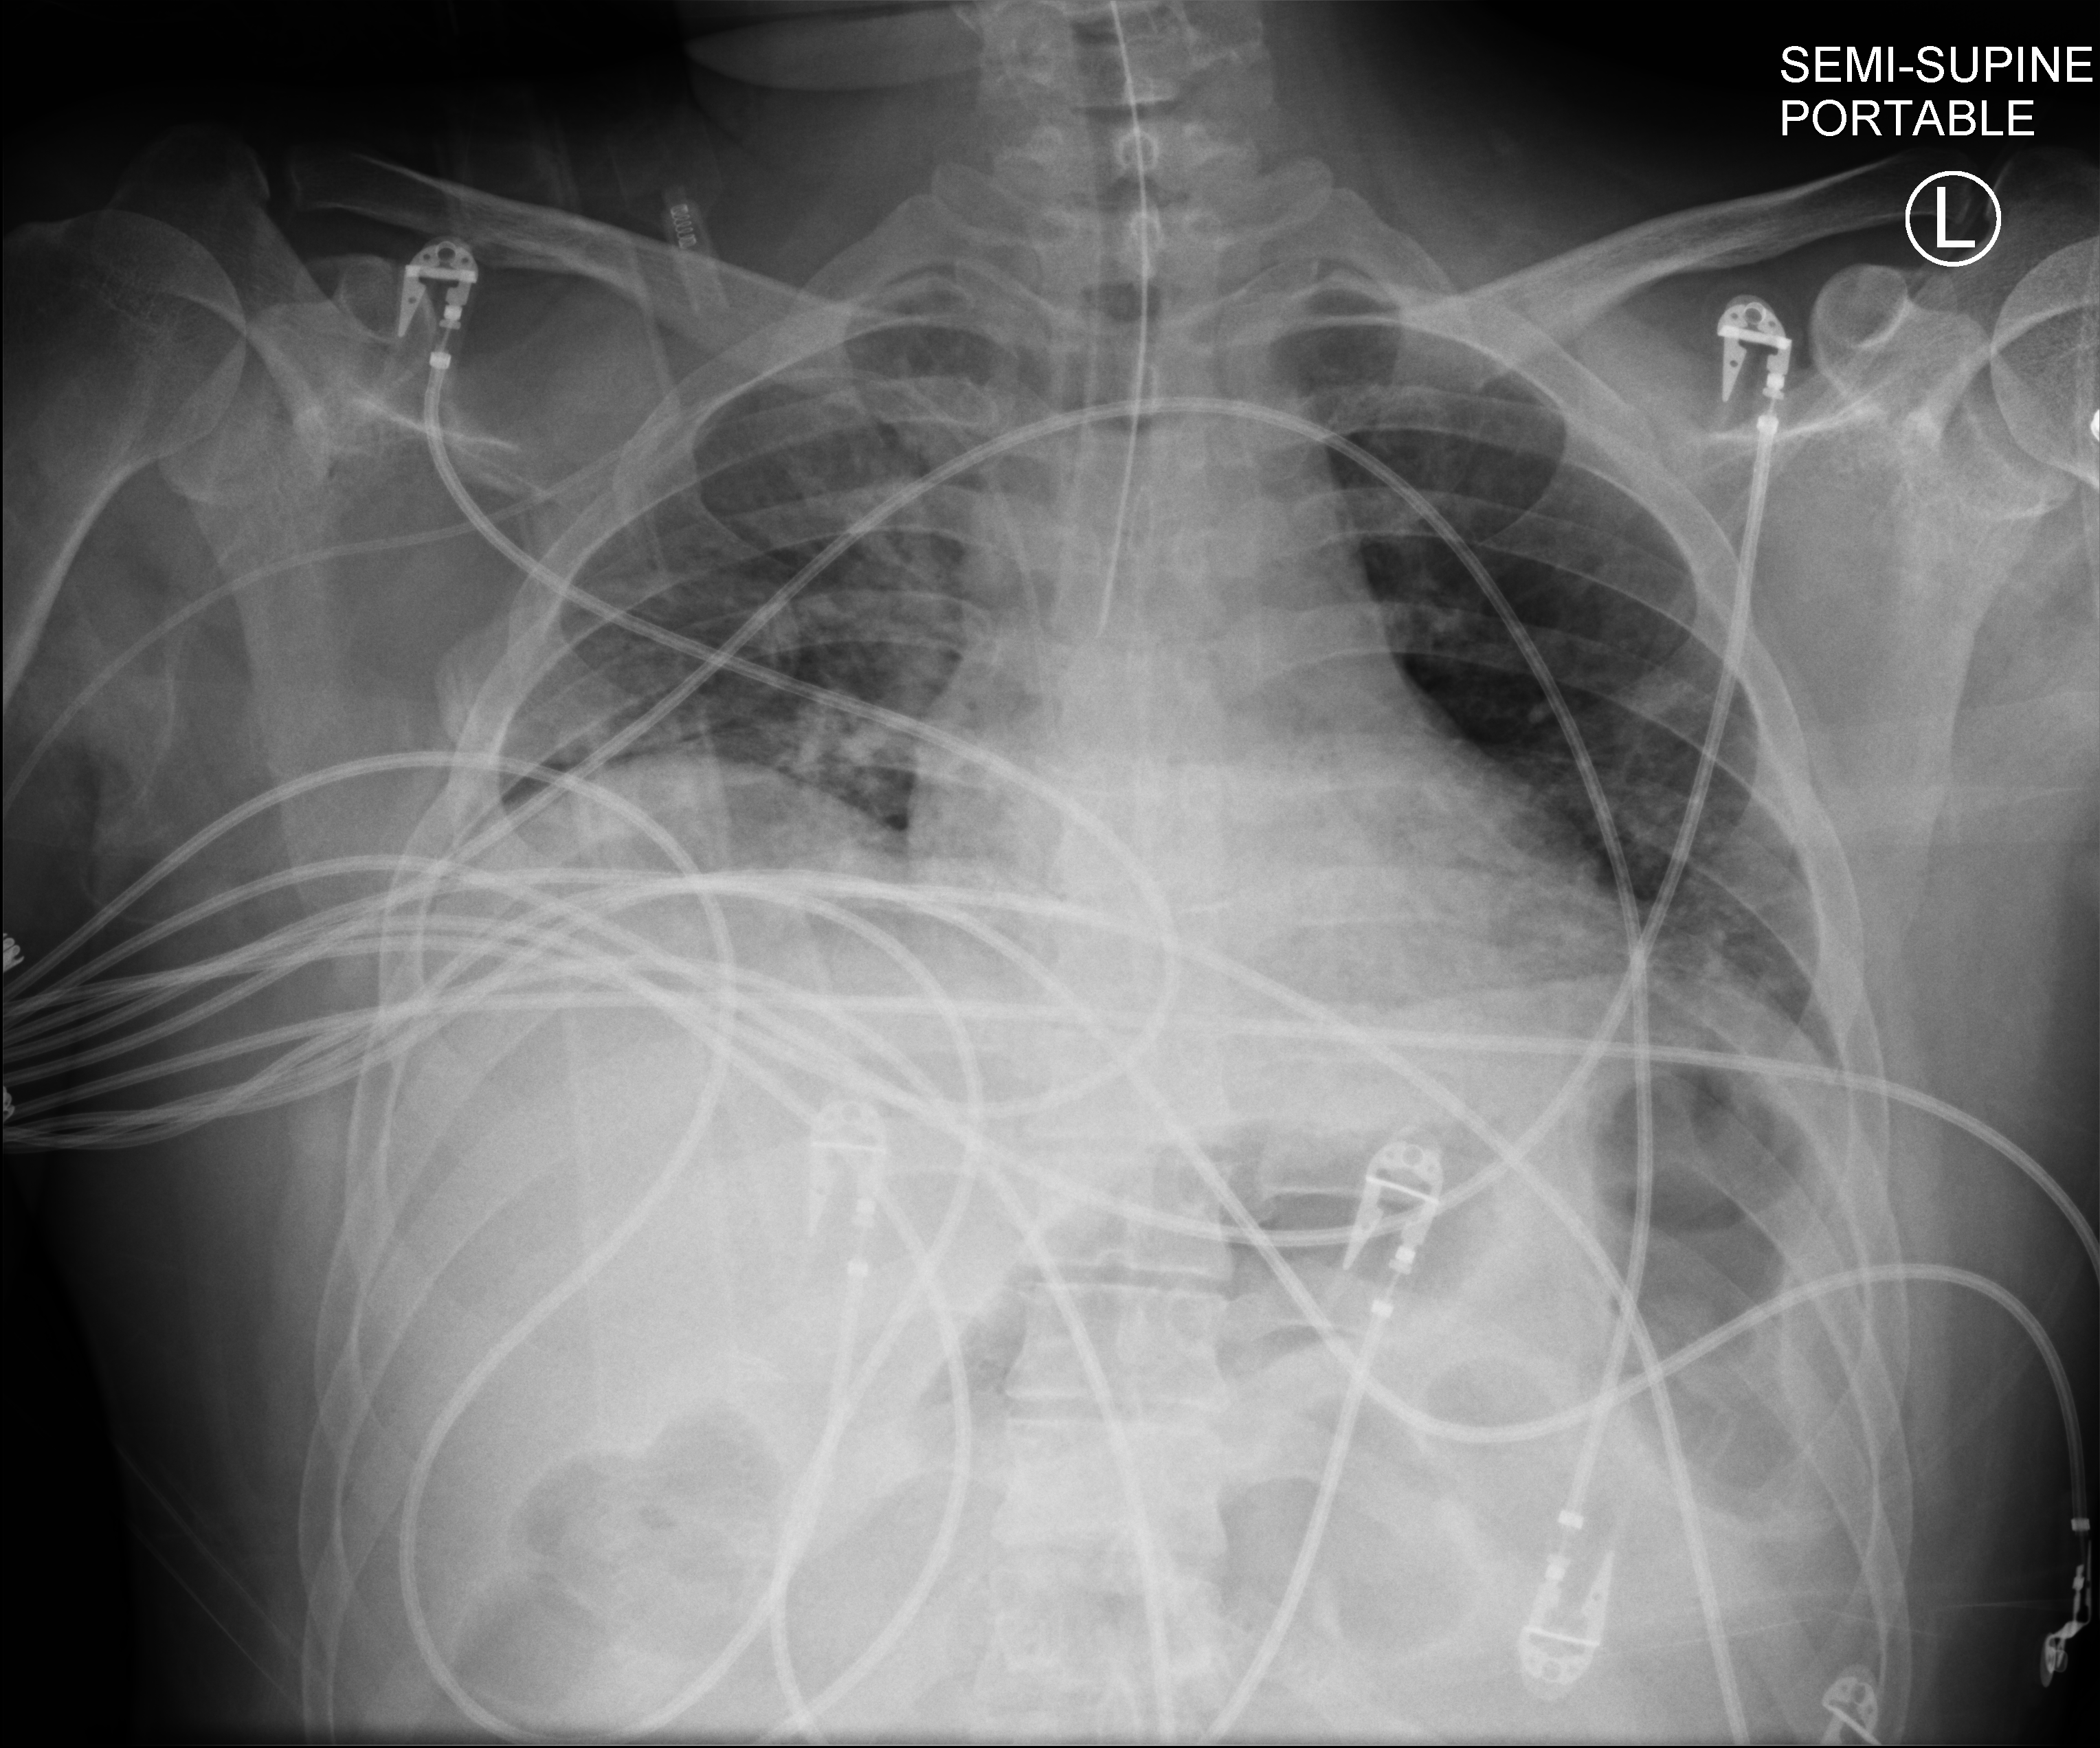
Bedside chest radiograph (computed radiography), anteroposterior (AP) projection. Male patient hospitalised with COVID-19, age 18–59 years.
Hospital-stay facts (about this admission, not read from this image; timing relative to this image not recorded): length of hospital stay: 44 days; mechanically ventilated during this hospital stay: yes.